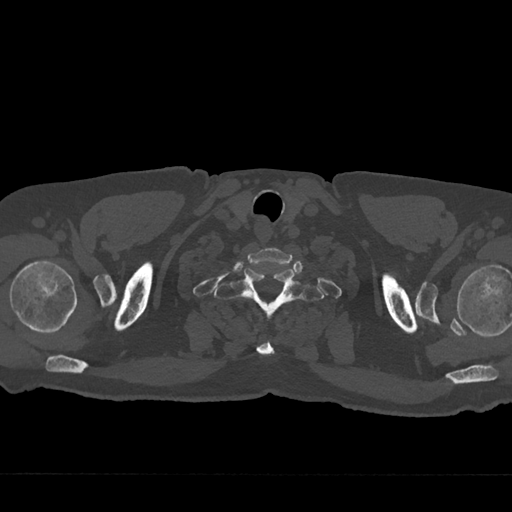
CT including the spine, one axial slice; slice 667 of 797 in the series (ordered by position); reconstruction kernel Br40s/3; bone window (W 1800 / L 400 HU); 0.5 mm slice thickness; 512 × 512 image matrix, field of view 377 × 377 mm. Male patient, age 75 years. From the clinical record (not read from this slice): primary cancer: renal; vertebrae with lytic lesions (as recorded): T4.
Annotated regions visible in this slice (semi-automatic segmentation, software-assisted and operator-edited):
- T1 vertebra: bounding box <214,268,324,355> (left, top, right, bottom; pixels)